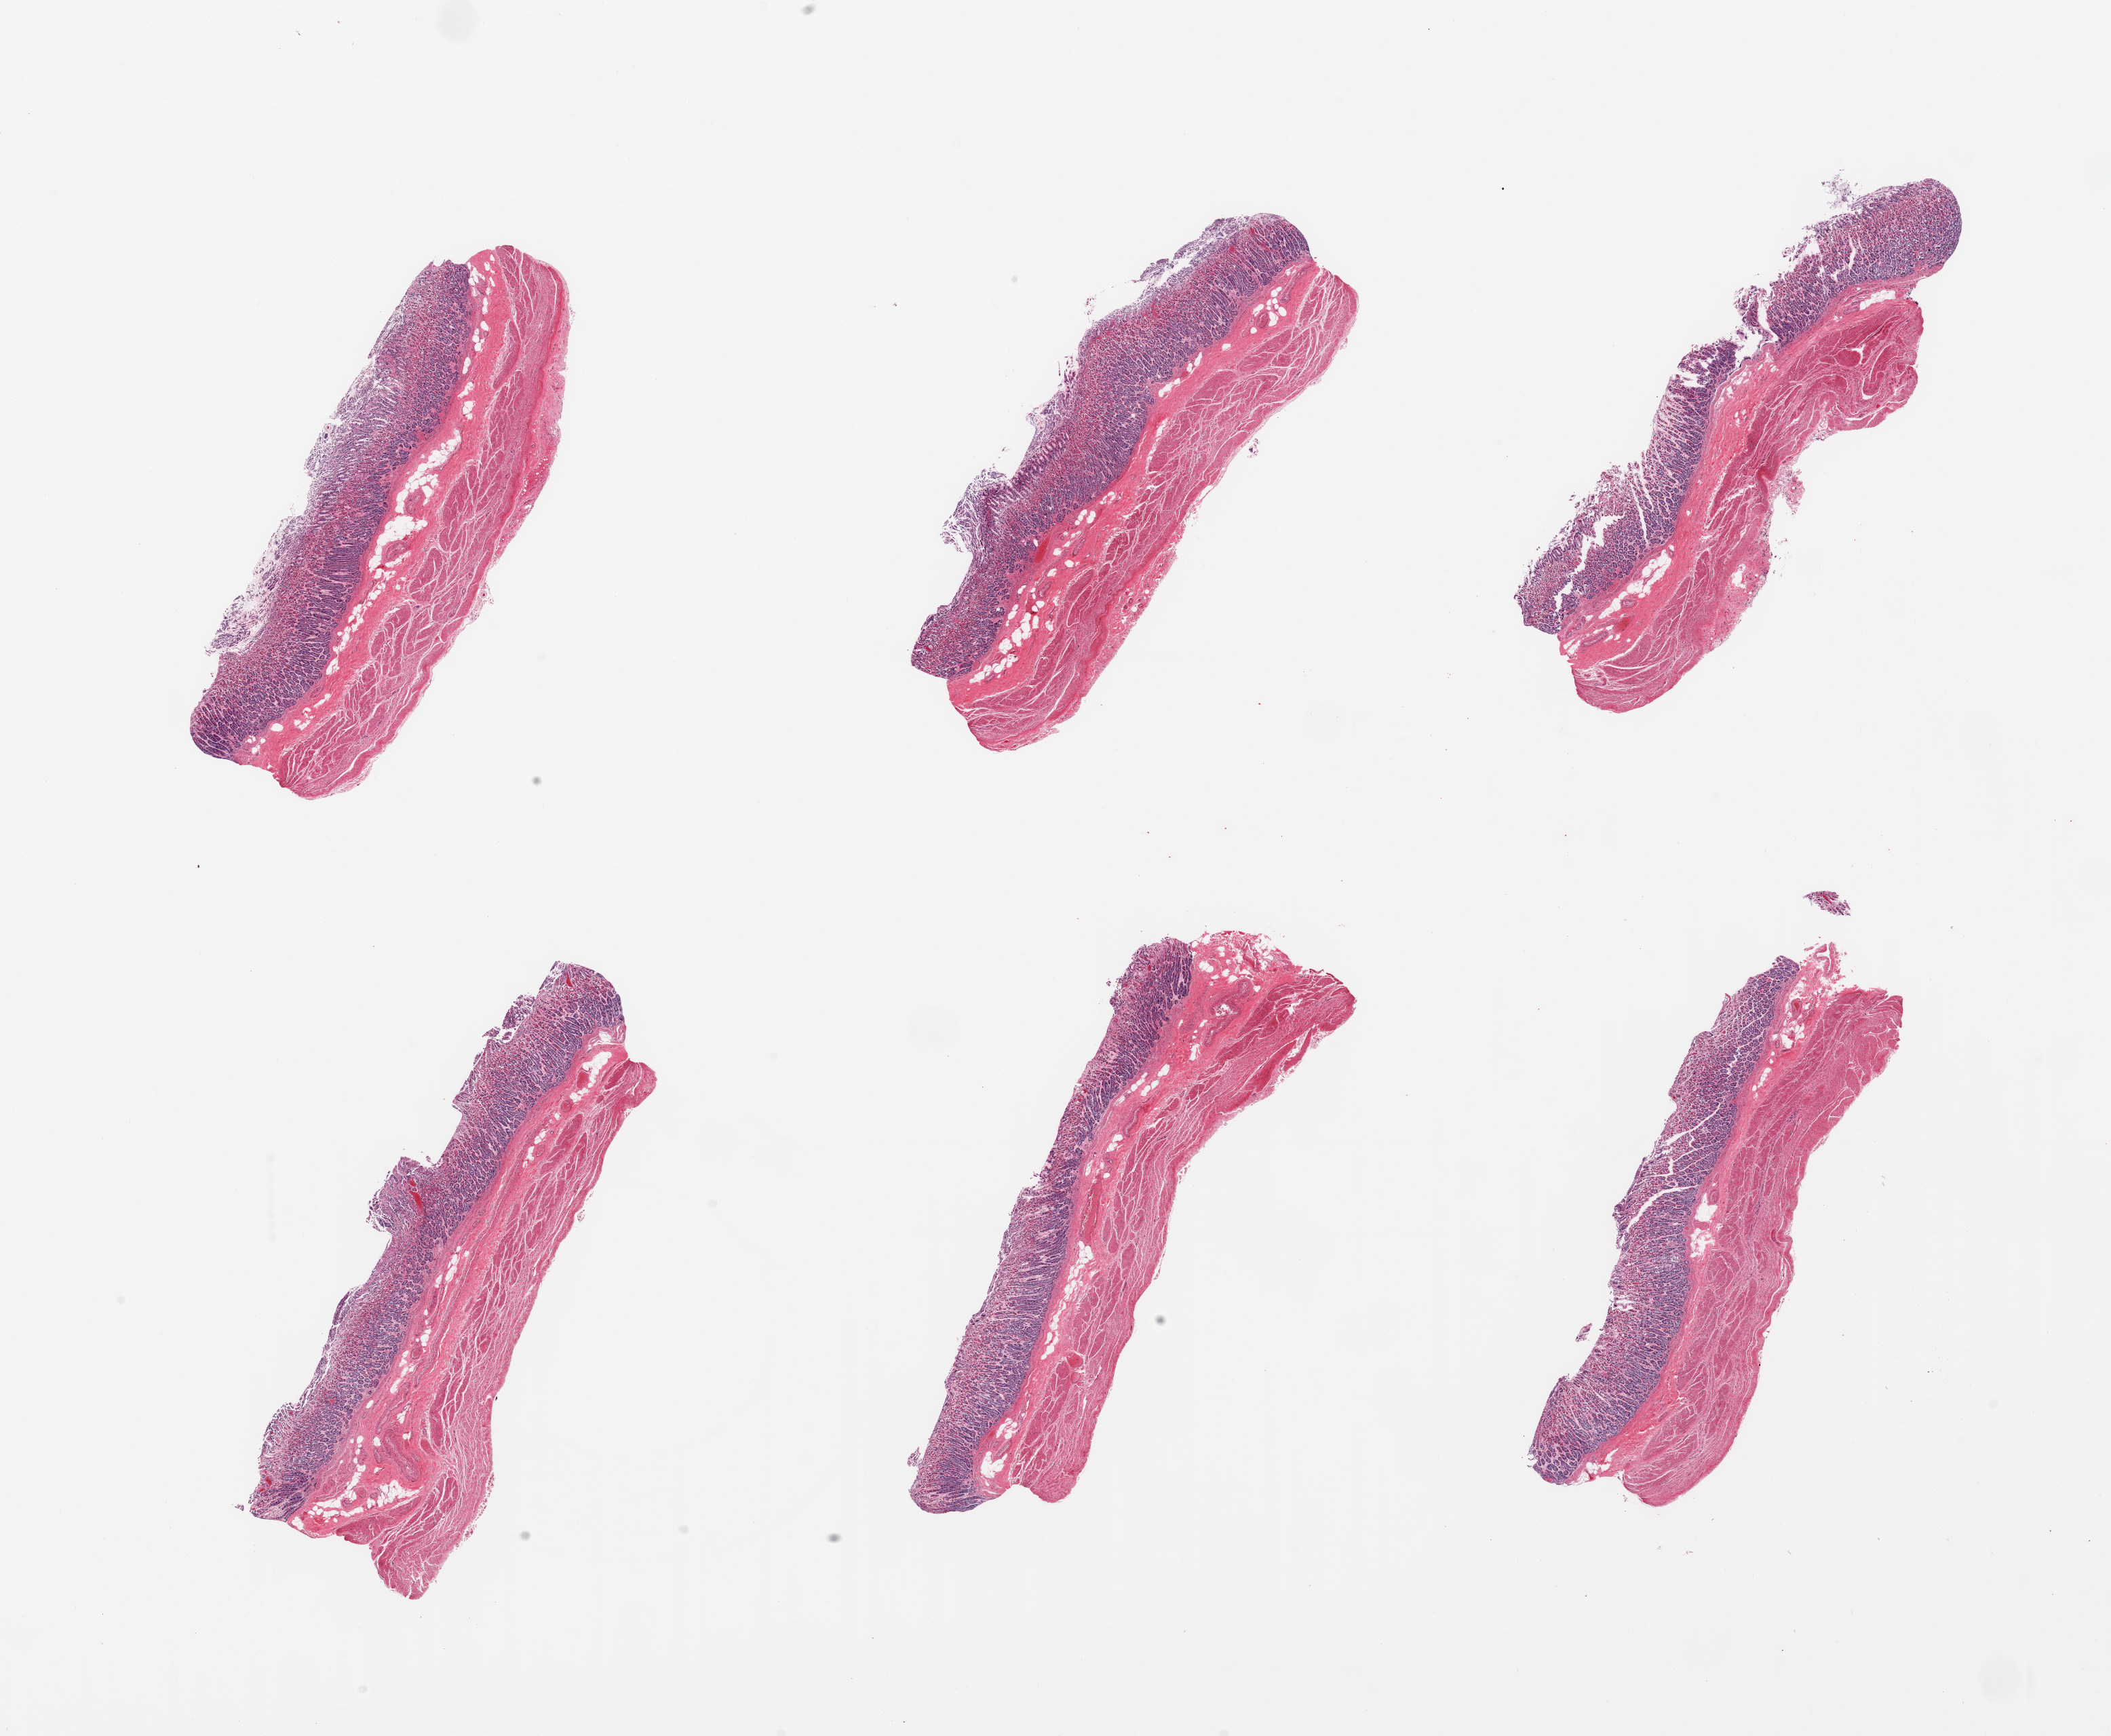
Whole-slide image, haematoxylin and eosin stain, brightfield — whole scanned area (about 24.6 x 20.2 mm, acquisition: 20x scan) shown as a low-resolution overview. PAXgene-fixed, paraffin-embedded tissue. Sampled site (target tissue): stomach. Donor tissue sample.
- pathologist's review note for this sample: 6 pieces; variable preservation of mucosa: superficial glands more autolyzed than deeper